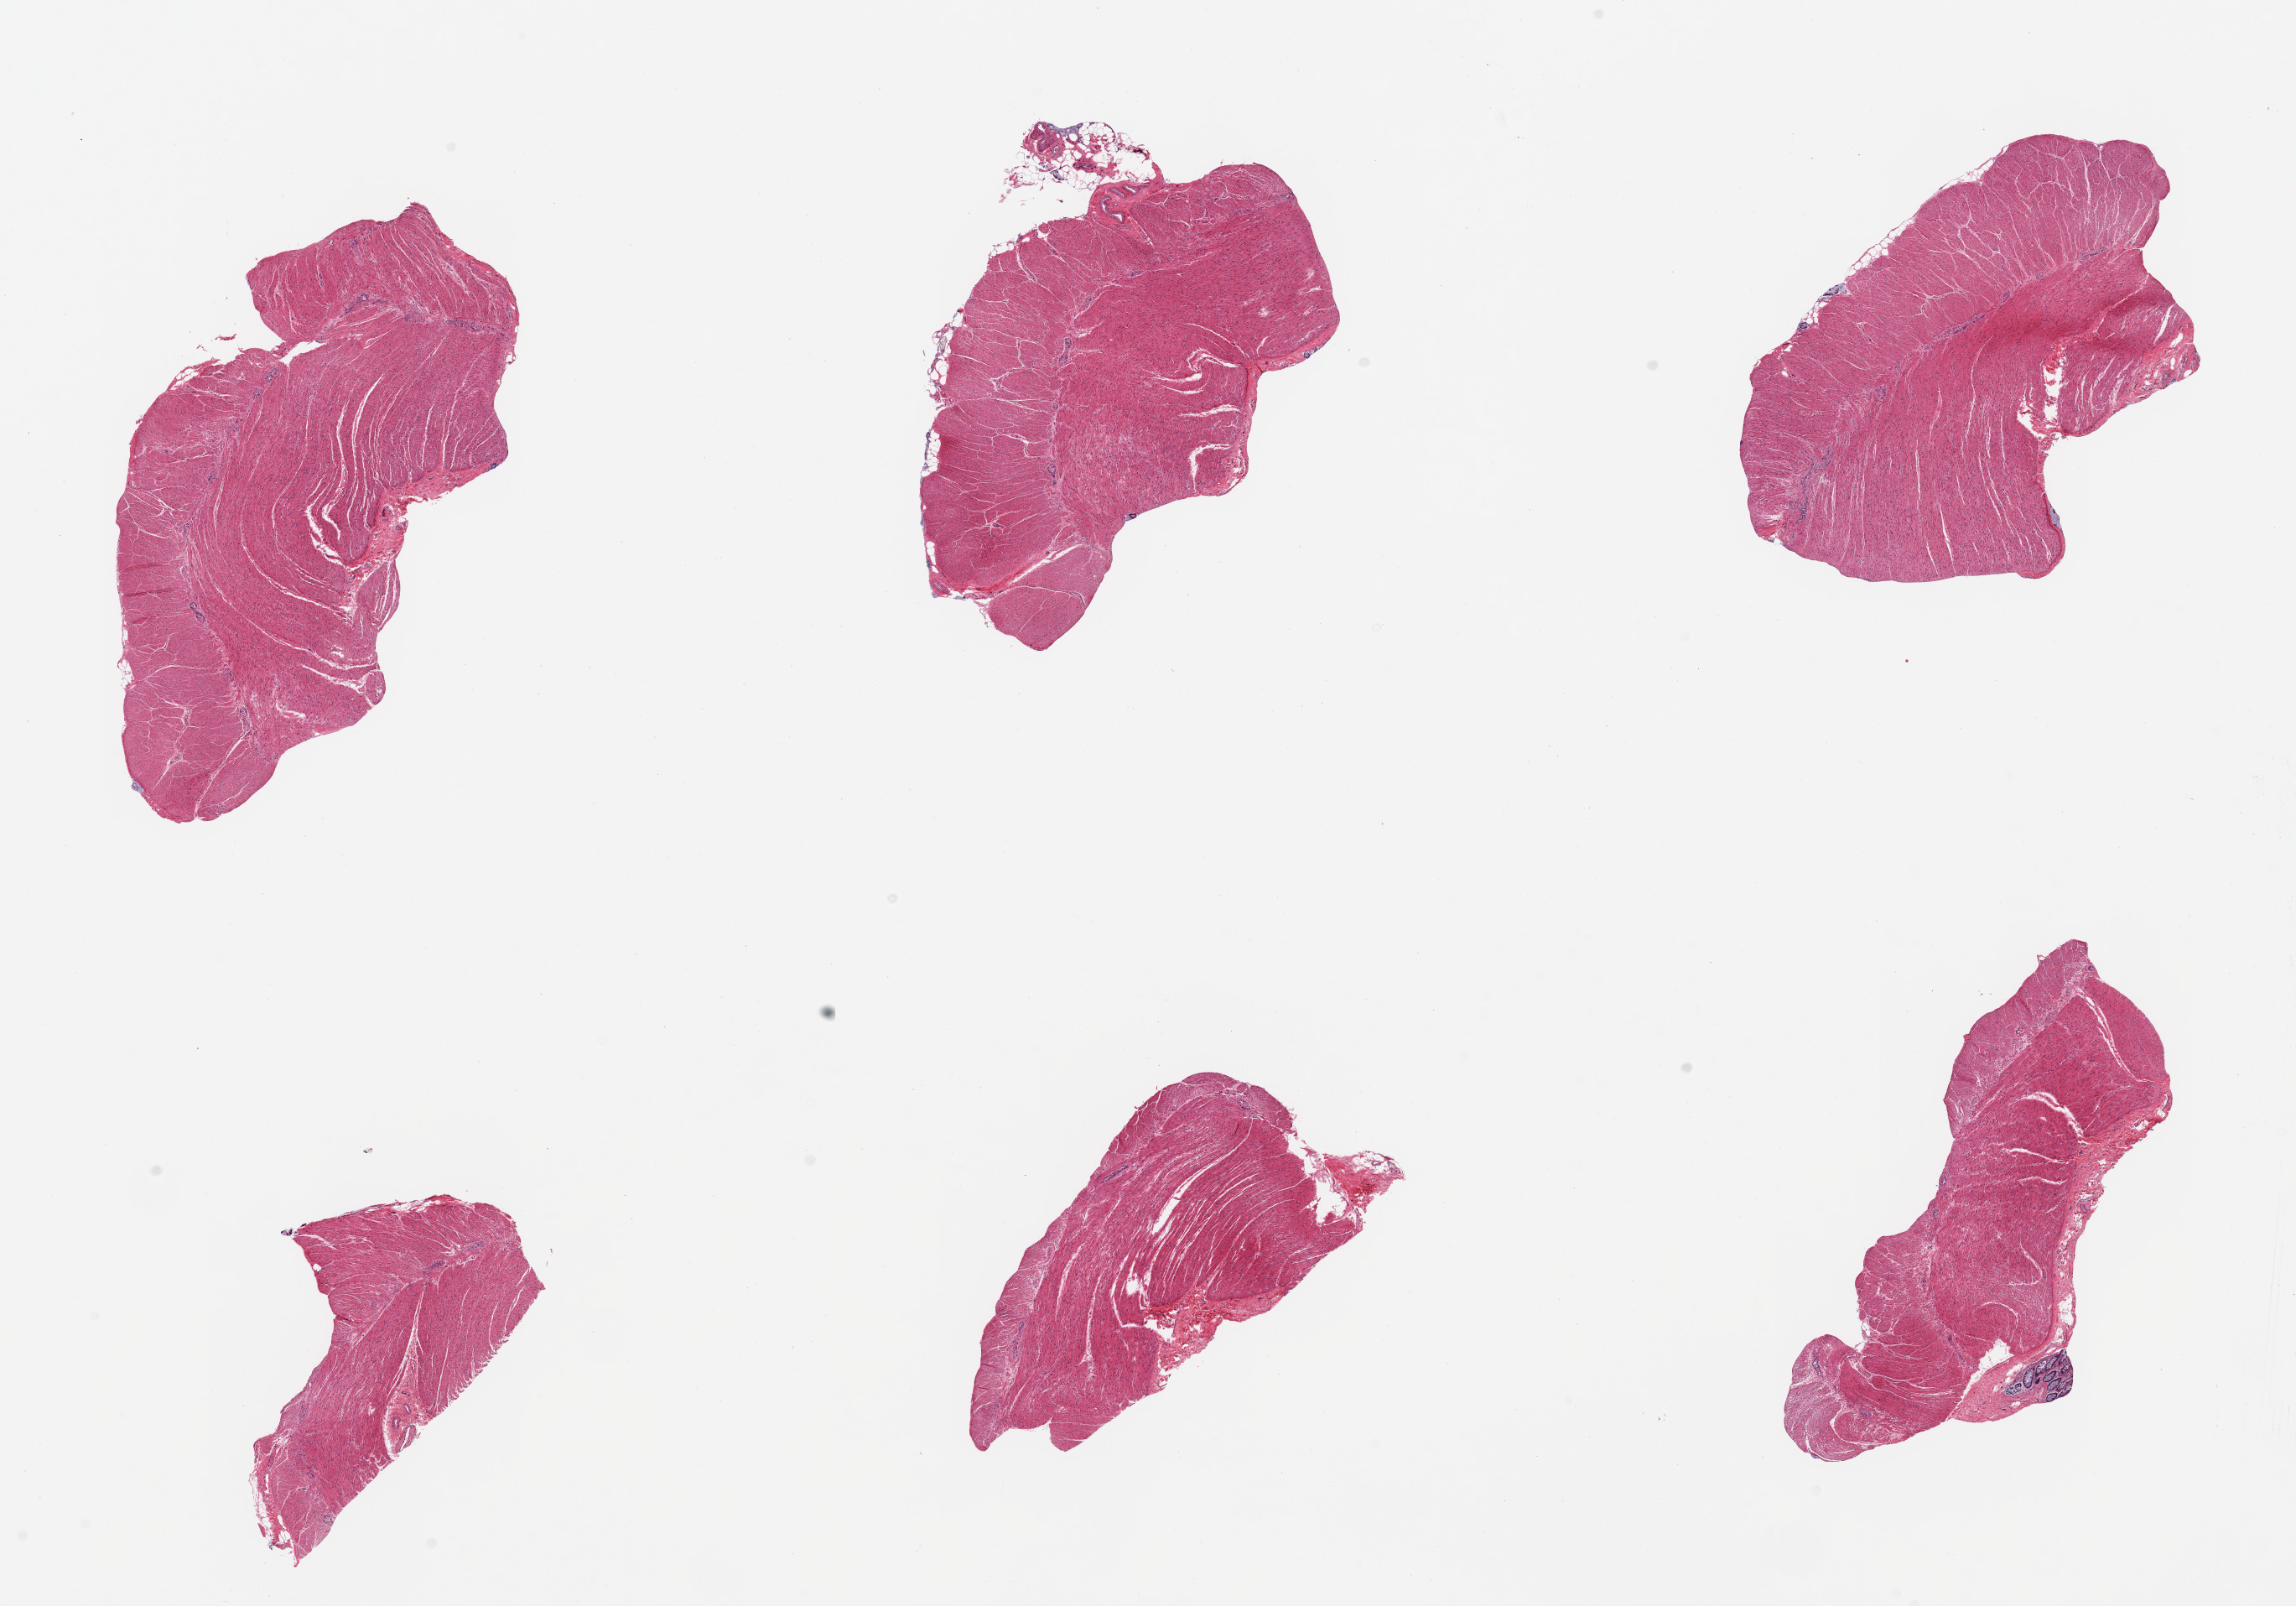
Whole-slide image, H&E stain — whole scanned area (about 21.7 x 15.1 mm) shown as a low-resolution overview; PAXgene-fixed, paraffin-embedded tissue; target tissue: sigmoid colon; tissue donor sample. Donor sex: female.
Review note (as recorded): 6 pieces; target muscularis with small focus of residual mucosa.